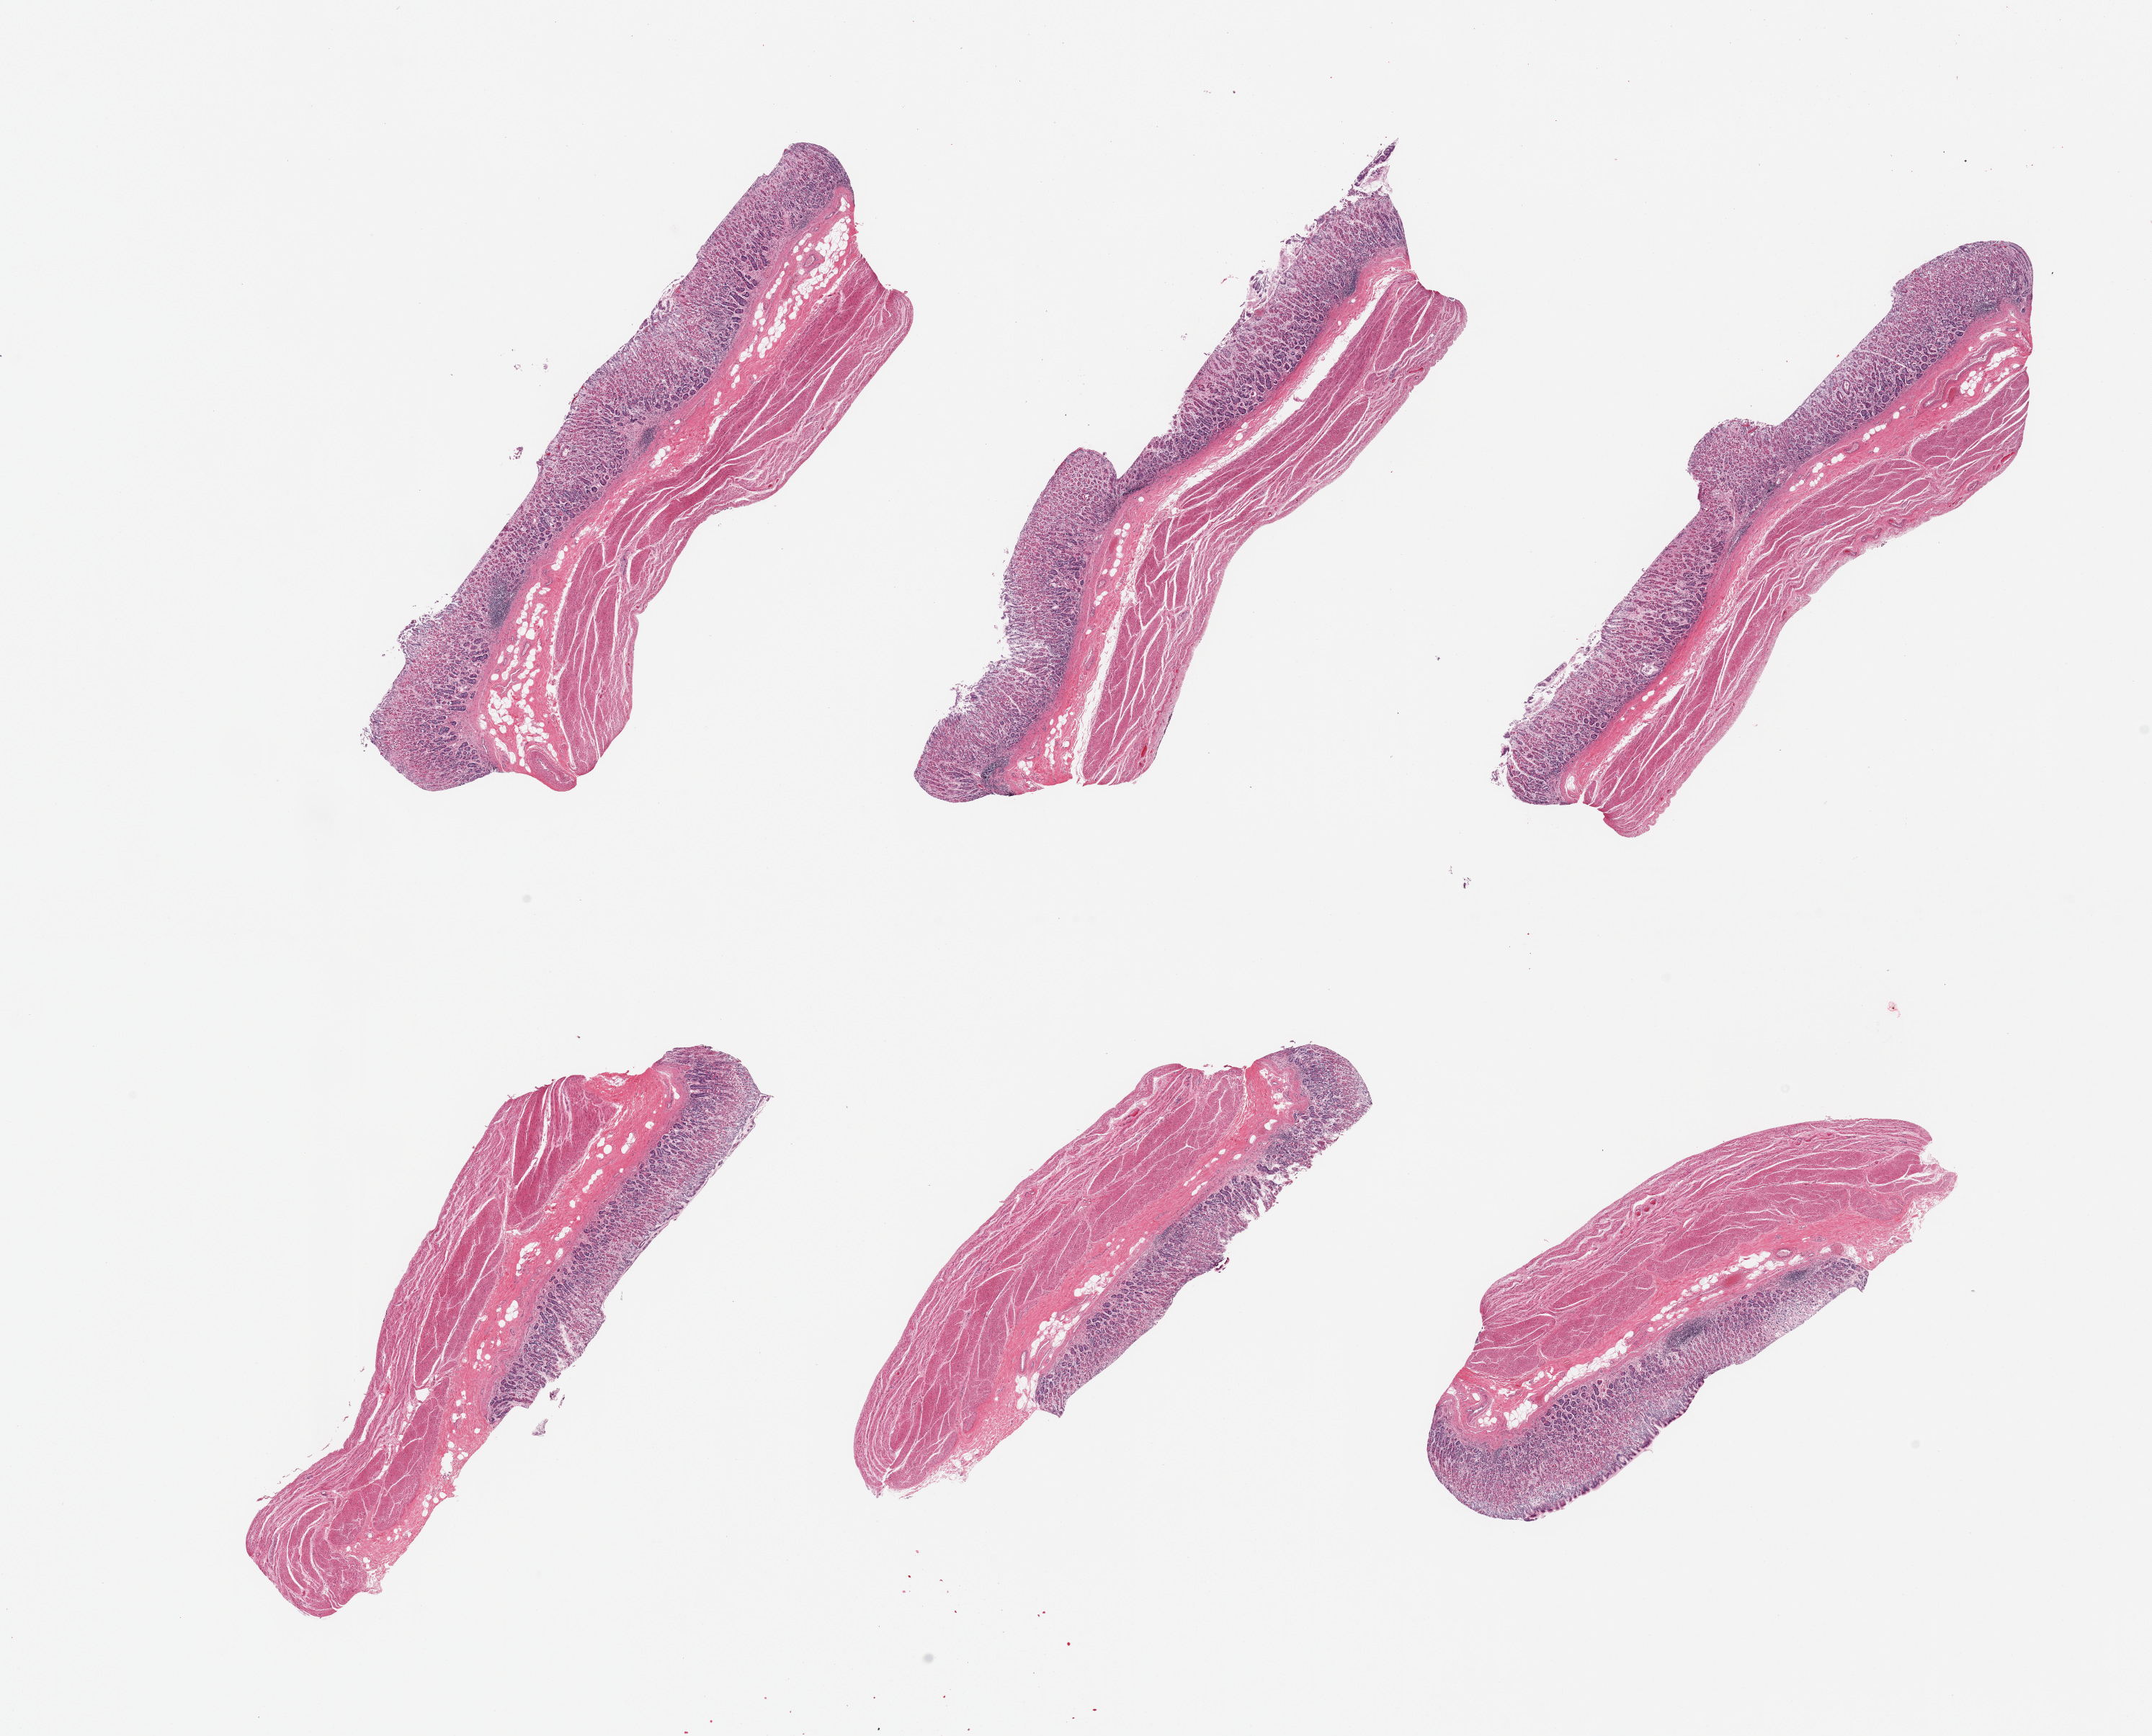
Whole-slide image, H&E stain, brightfield — low-resolution overview of the scanned area, about 23.6 x 19.1 mm; PAXgene-fixed, paraffin-embedded tissue; sampled site (target tissue): stomach; donor tissue sample. Donor: female.
Review note (as recorded): 6 pieces; moderate superficial mucosal autolysis; muscle intact.